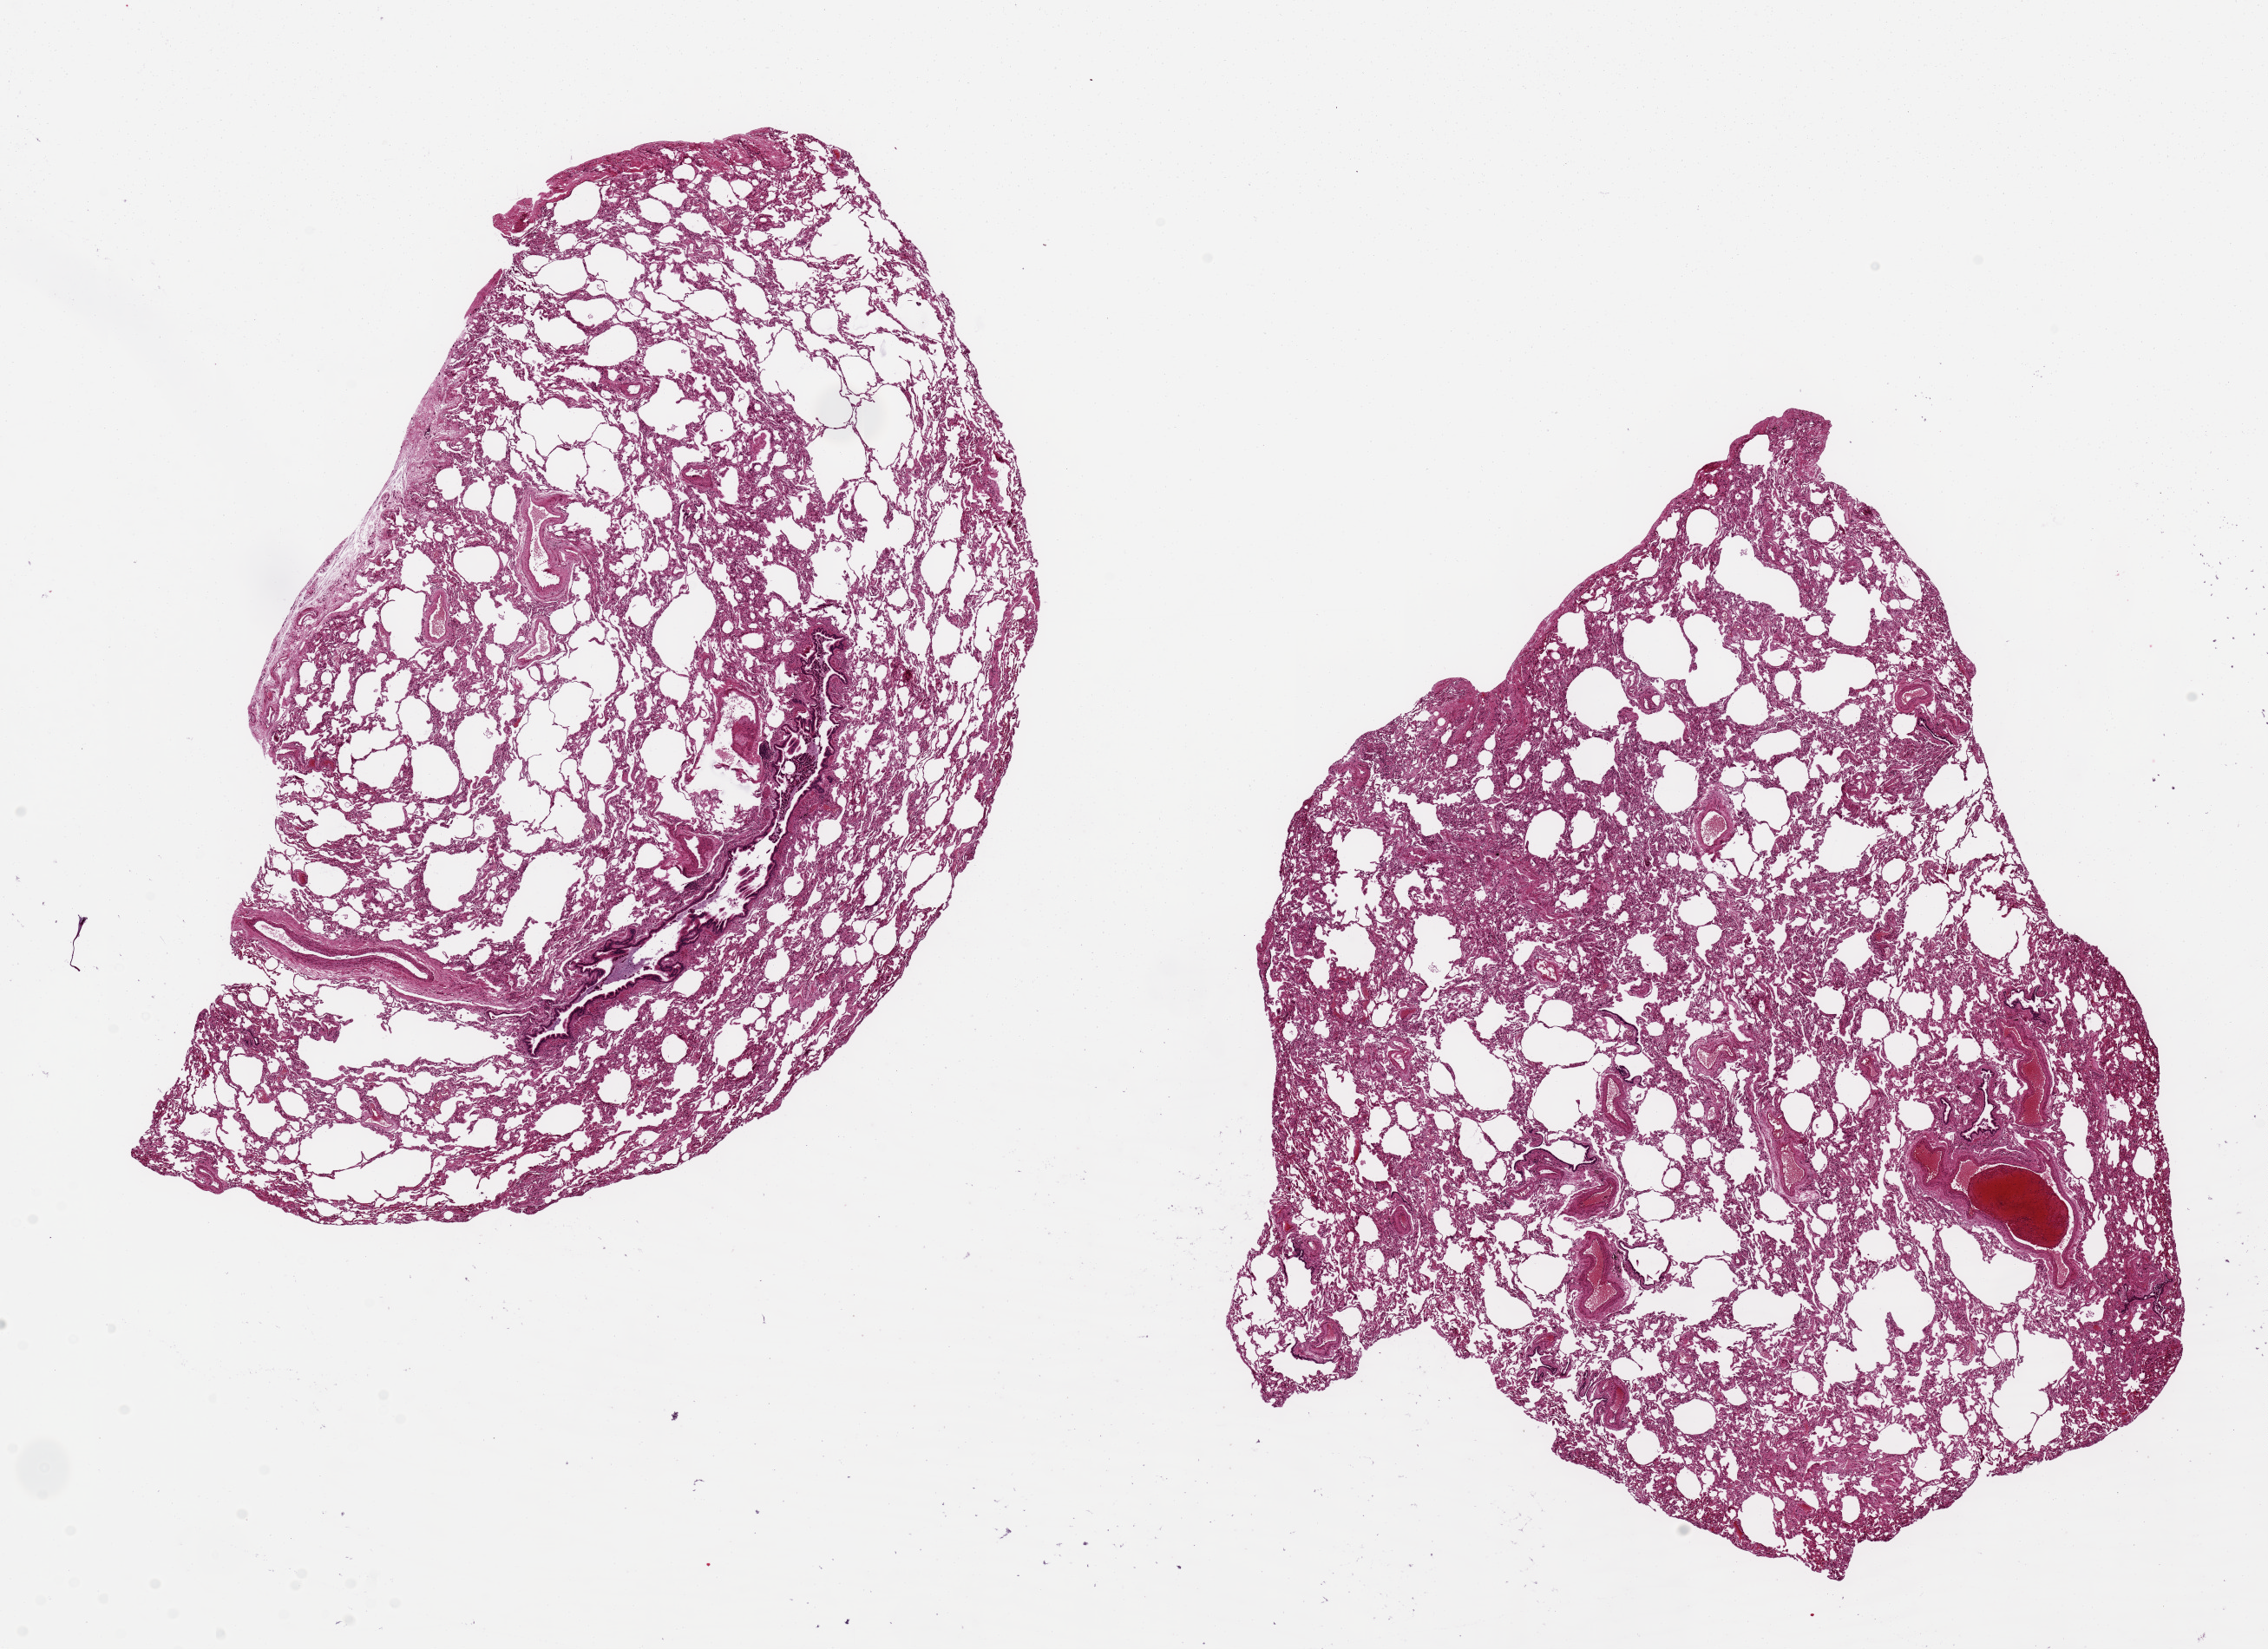
Hematoxylin and eosin (H&E) whole-slide image, brightfield — low-resolution overview of the scanned area, about 20.7 x 15.0 mm. PAXgene-fixed paraffin-embedded (PFPE) section. Sampled site (target tissue): lung. Donor tissue sample. Female donor.
• pathologist's review note for this sample: 2 pieces, 11x6 & 9x9 mm; no inflammation